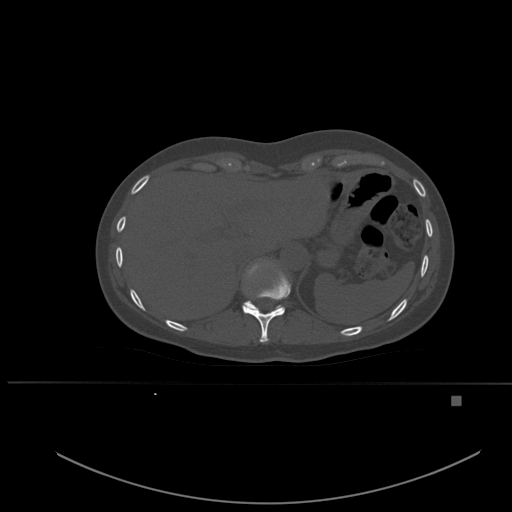
CT including the spine, one axial slice; position 284 of 651 along the scan axis; bone window (W 1800 / L 400 HU); 1.5 mm slice thickness; 512 × 512 image matrix, field of view 443 × 443 mm. Patient: female, 49 years. Case-level facts recorded for this patient, not image findings: primary cancer: breast.
Annotated regions visible in this slice (semi-automatically segmented with operator editing):
- T10 vertebra: bounding box <242,270,291,343> (left, top, right, bottom; pixels)
- T11 vertebra: <245,263,282,311>